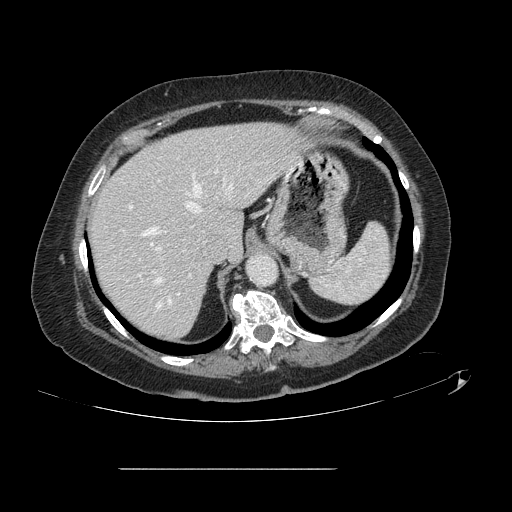
Contrast-enhanced abdominal CT, one axial slice. Position 102 of 148 along the scan axis. 120 kVp. Intravenous contrast given. Soft-tissue window (W 400 / L 40 HU). 2.5 mm slice thickness. 512 × 512 image matrix. Female patient, age 75 years. Case-level facts recorded for this patient, not image findings: diagnosis: colorectal cancer liver metastases, imaged before liver resection; multiple liver metastases: no; largest metastasis: 2.4 cm; disease in both lobes: no.
Annotated regions visible in this slice (expert manual segmentation):
- hepatic veins: box from (x=141, y=169) to (x=234, y=307) px
- liver: (x=90, y=123)–(x=304, y=339)
- planned liver remnant (the part of the liver to remain after resection): (x=90, y=123)–(x=304, y=339)
- portal vein (with intrahepatic branches): (x=129, y=181)–(x=160, y=250)